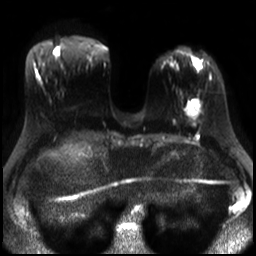
Breast MRI, one axial slice. Position 8 of 30 along the scan axis. Diffusion-weighted series; image 2 of 4 stored at this slice position (different b-values; order by instance number). 3 T. 256 × 256 image matrix, field of view 320 × 320 mm. Female patient.
Annotated regions visible in this slice (expert manual segmentation):
- tumour on diffusion-weighted imaging: bounding box <187,99,201,118> (left, top, right, bottom; pixels)